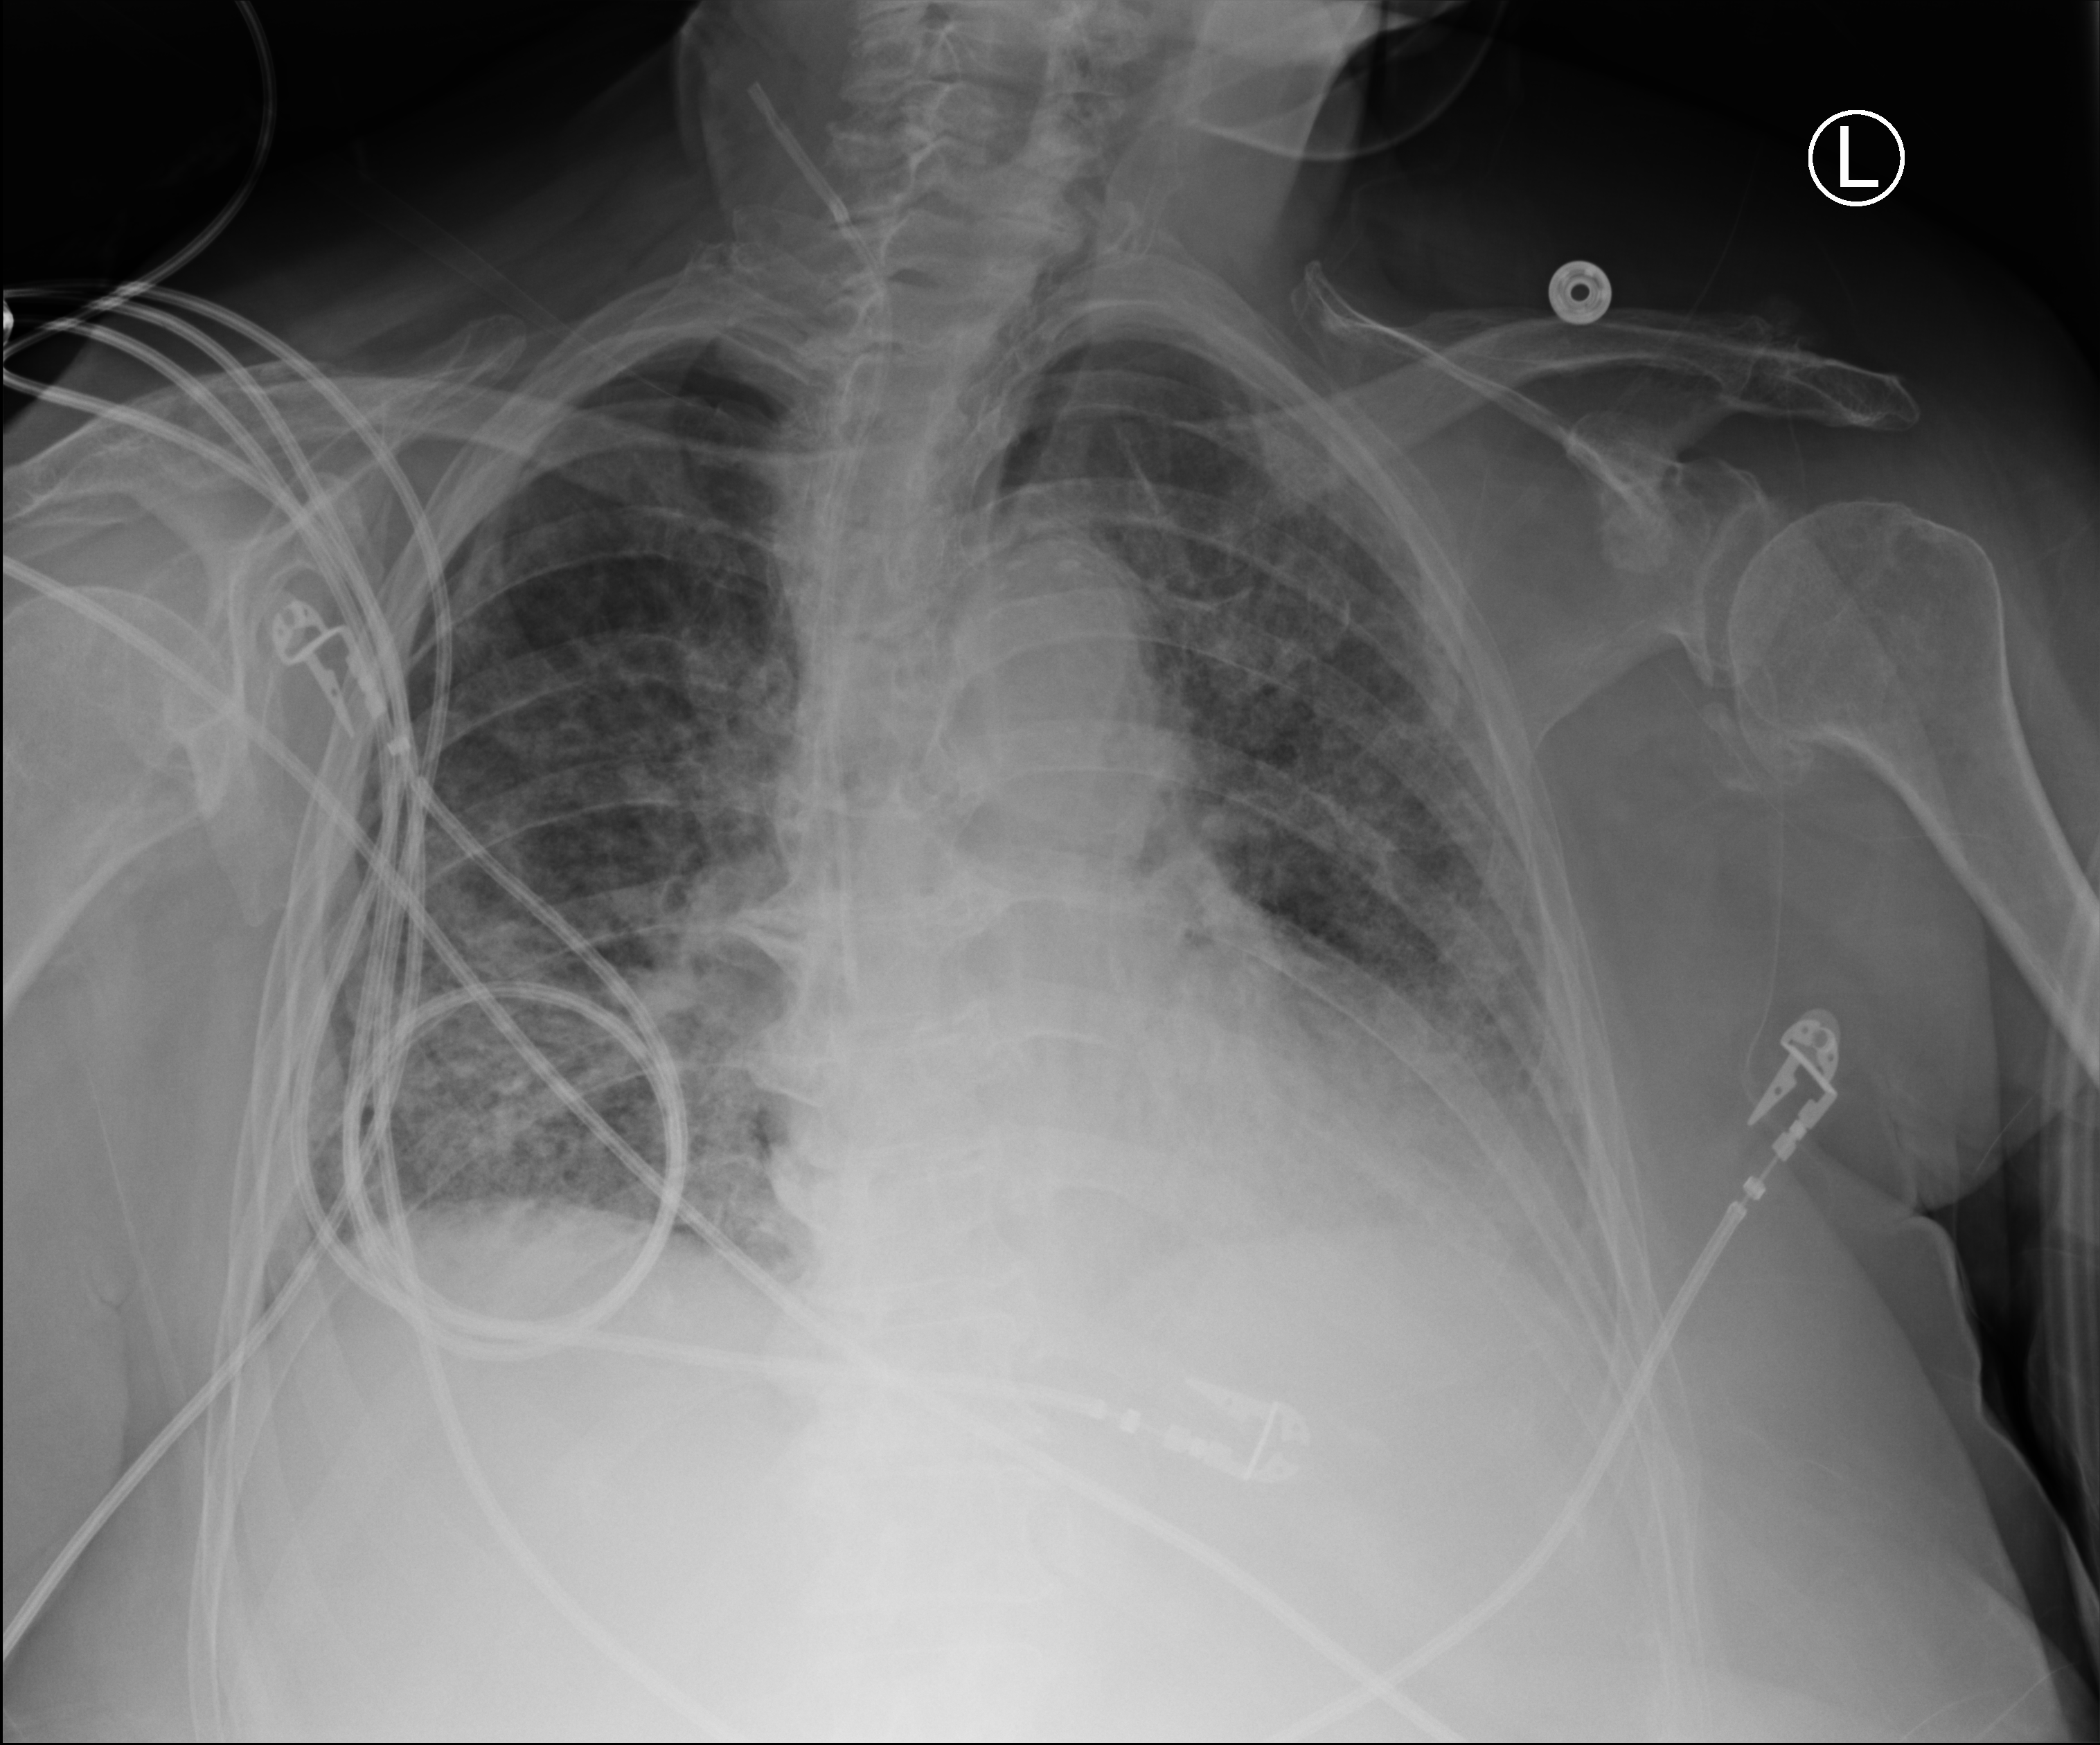
Bedside chest radiograph (computed radiography); anteroposterior (AP) projection. Patient hospitalised with COVID-19; female, aged 75–90 years.
Hospital-stay facts (about this admission, not read from this image; timing relative to this image not recorded):
- admitted to intensive care during this hospital stay: no
- hypertension (admission record): no
- other chronic lung disease (admission record): no